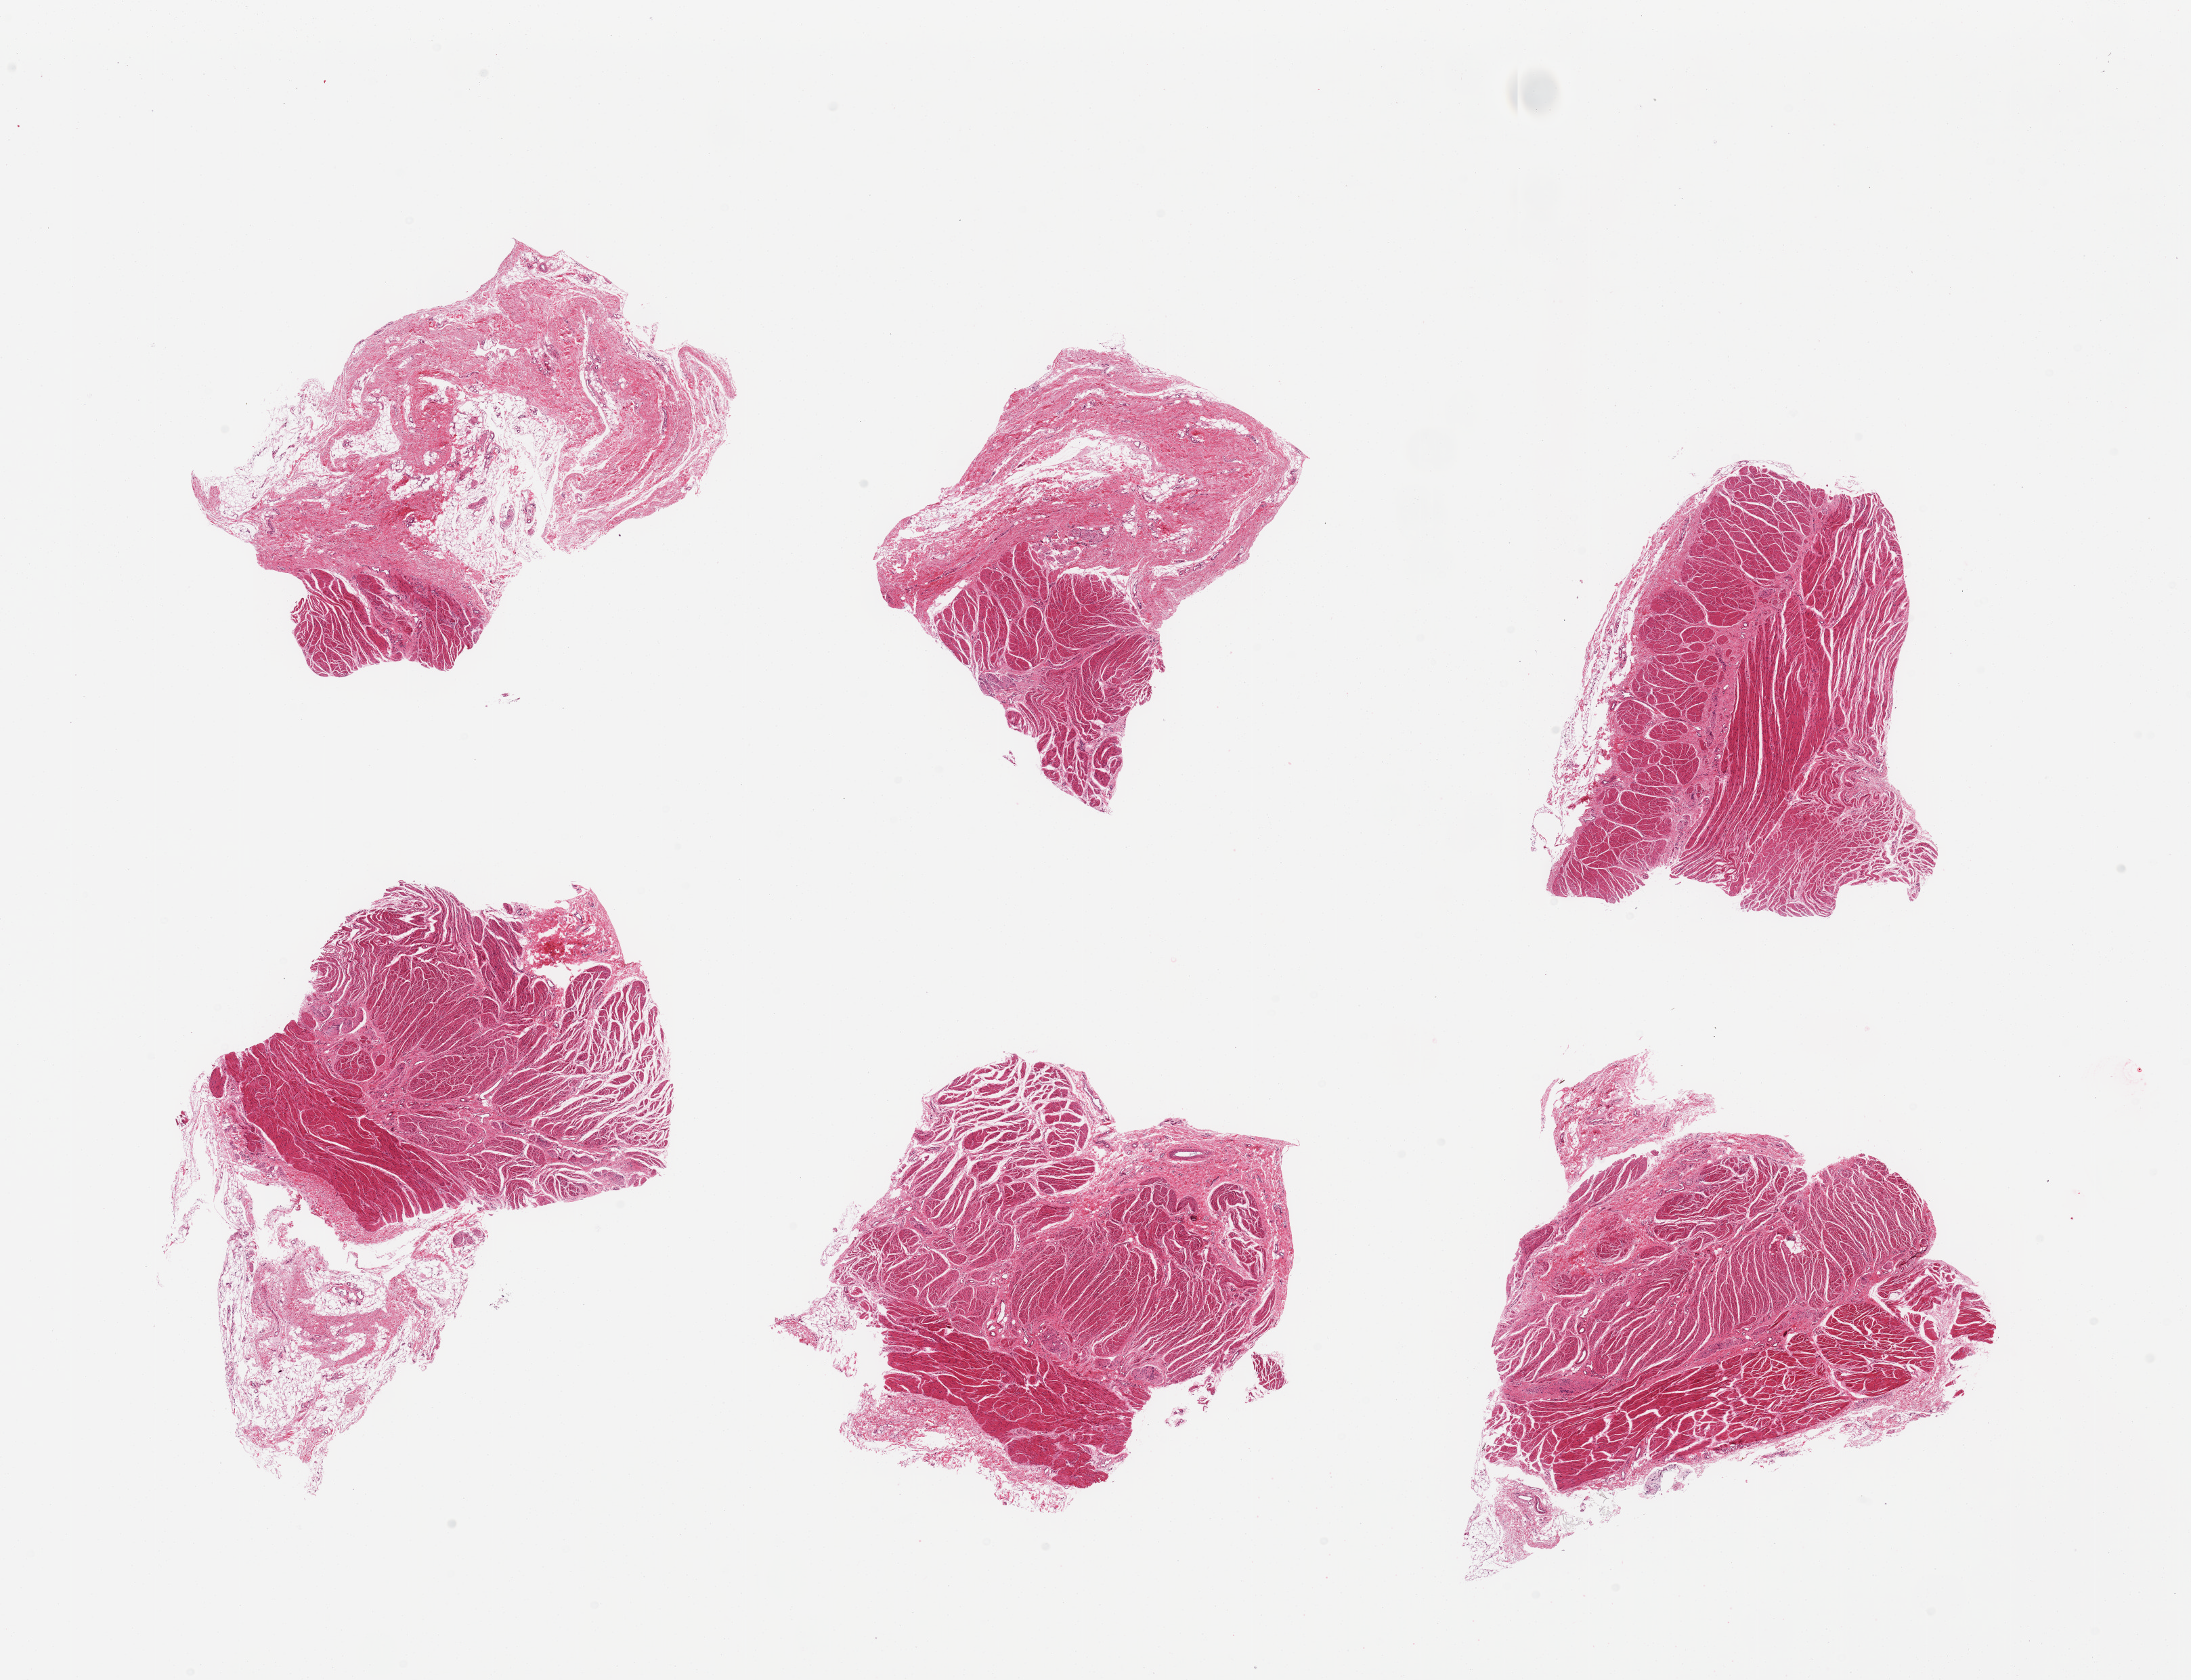
Whole-slide image, H&E stain — low-resolution overview of the scanned area, about 25.6 x 19.6 mm. PAXgene-fixed, paraffin-embedded tissue. Sampled site (target tissue): gastroesophageal junction. Donor tissue sample. Donor: male.
• pathologist's review note for this sample: 6 pieces; target muscularis; attached serosa